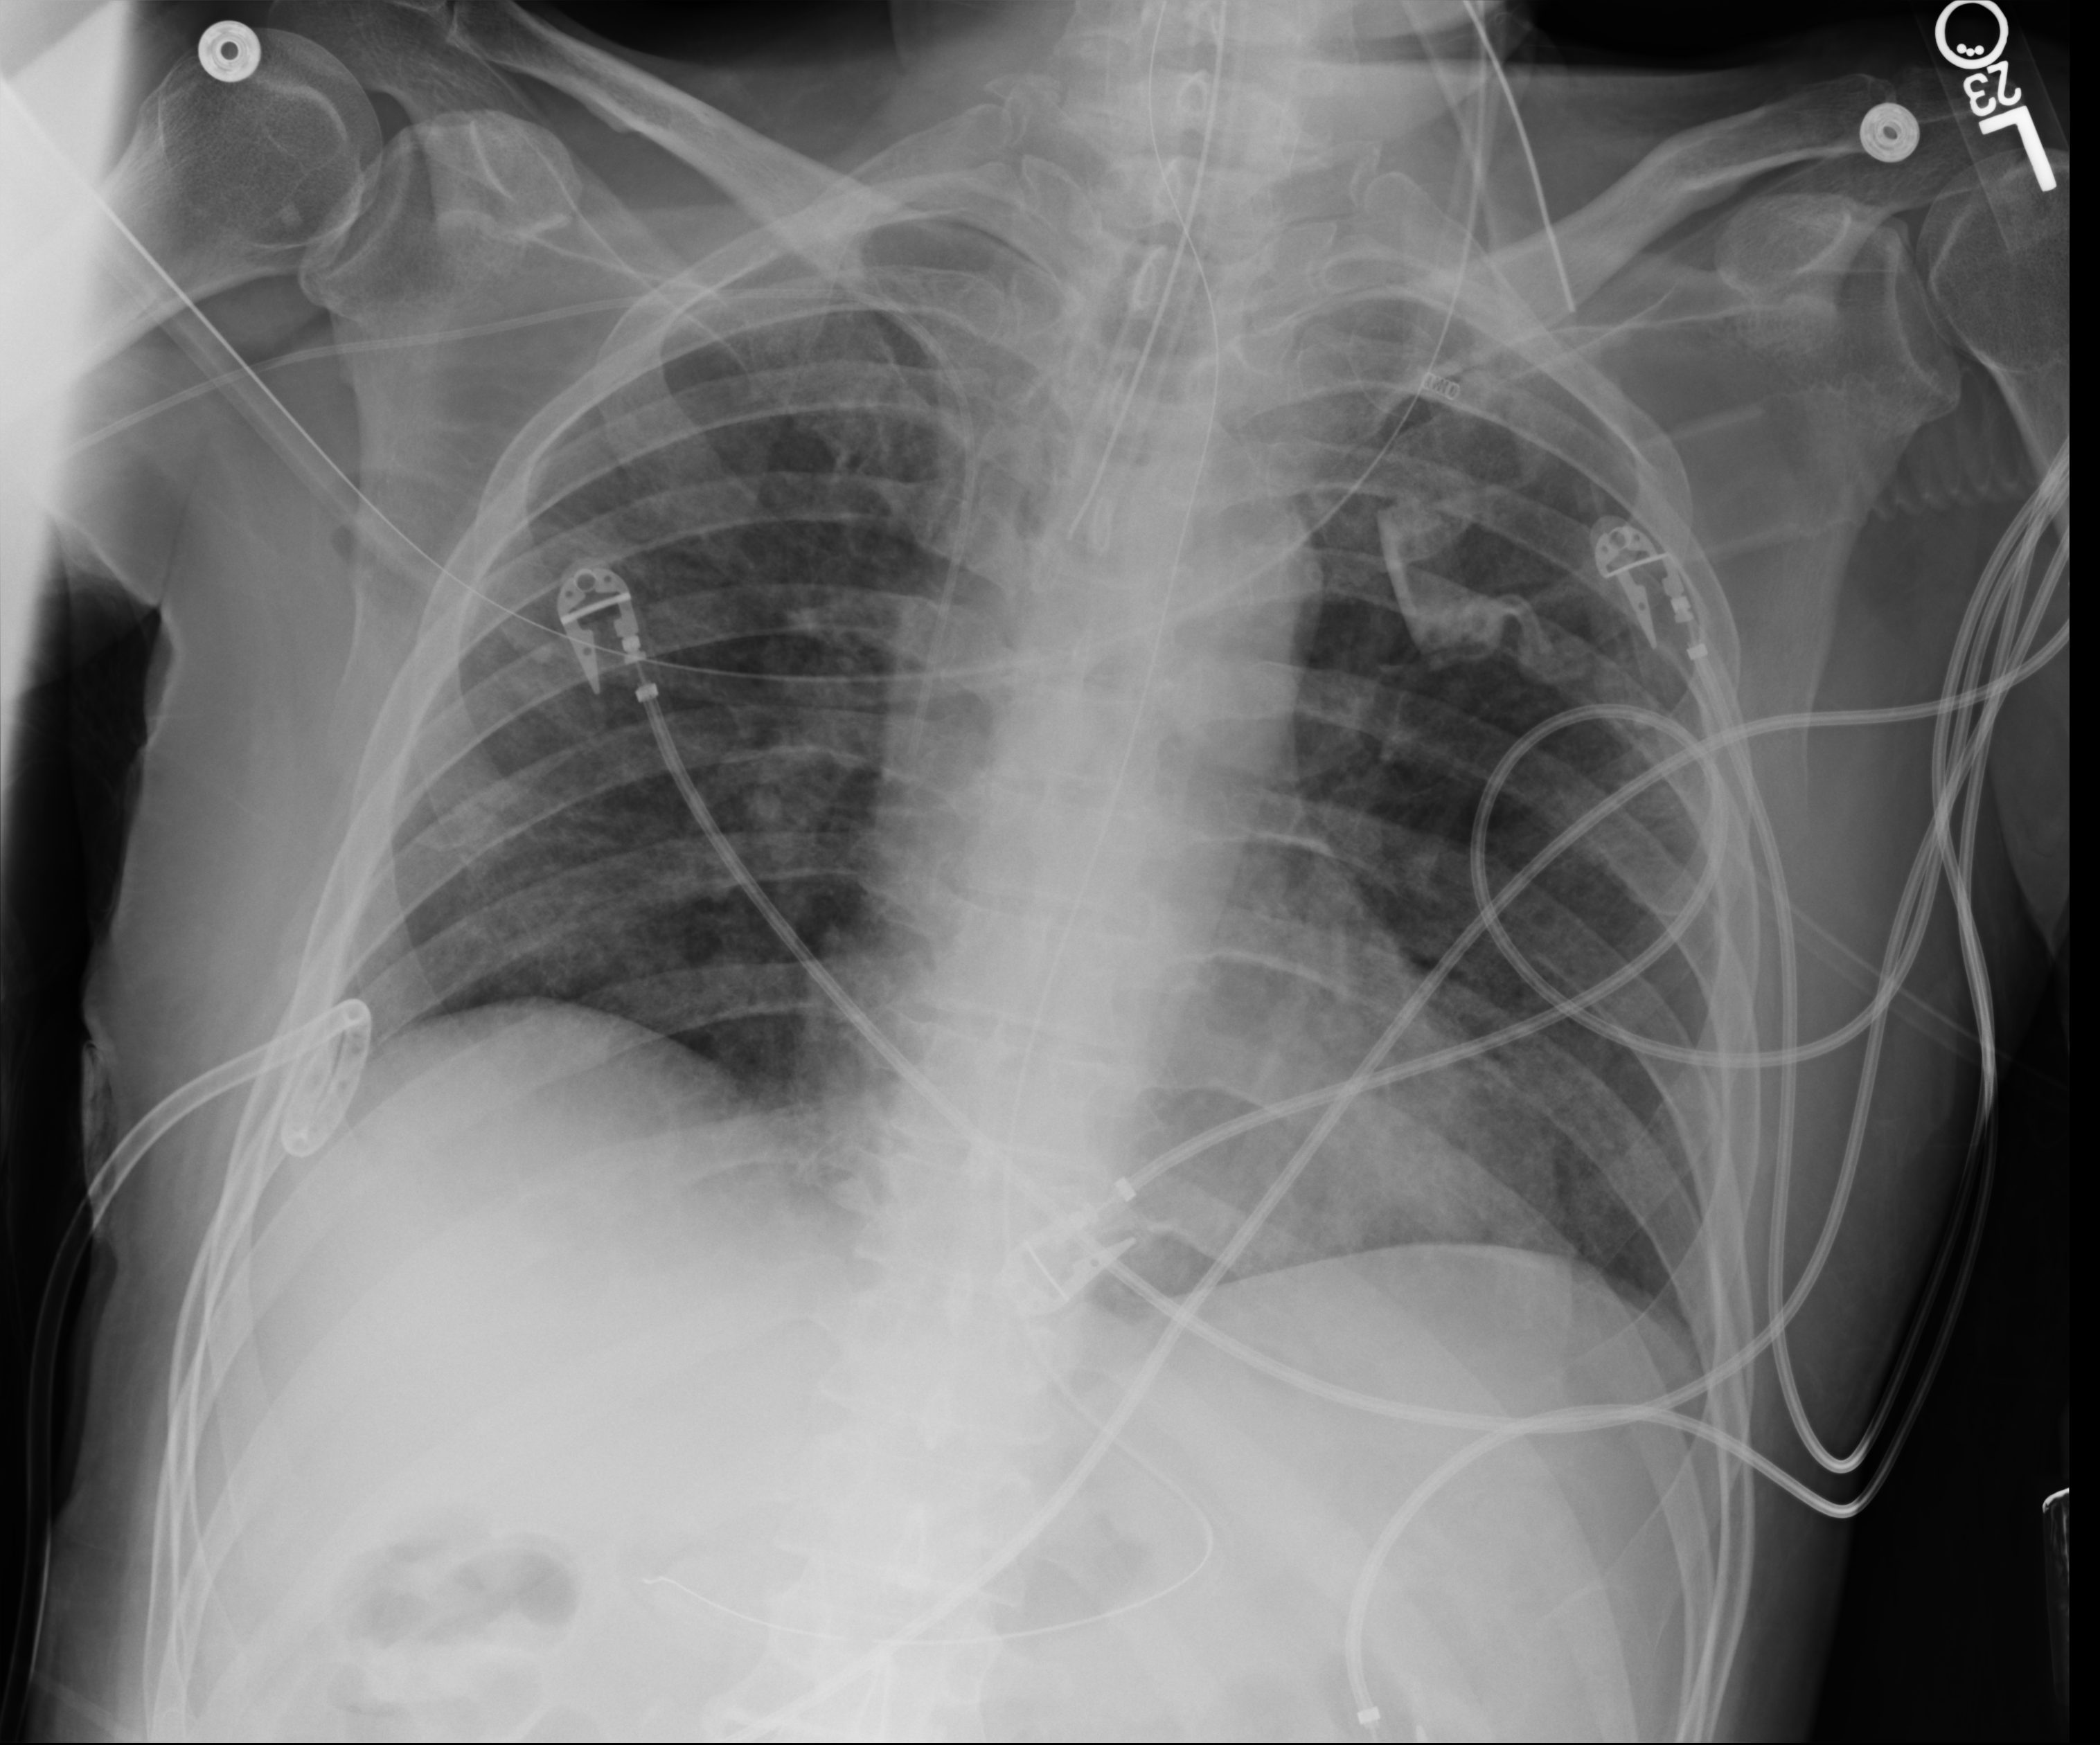
Chest X-ray (portable). Patient hospitalised with COVID-19; male, aged 18–59 years.
Admission-level facts for this patient (not findings on this image; timing relative to this image not recorded):
- mechanically ventilated during this hospital stay: yes
- diabetes (admission record): no
- admitted to intensive care during this hospital stay: yes